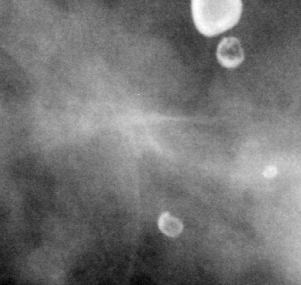
Region of interest cut from a scanned film mammogram (one marked finding); left breast; MLO view; BI-RADS breast density category 2 (scale 1–4).
- Marked abnormality: mass, shape architectural distortion, margins spiculated; BI-RADS assessment category 4; pathology (as recorded): benign.